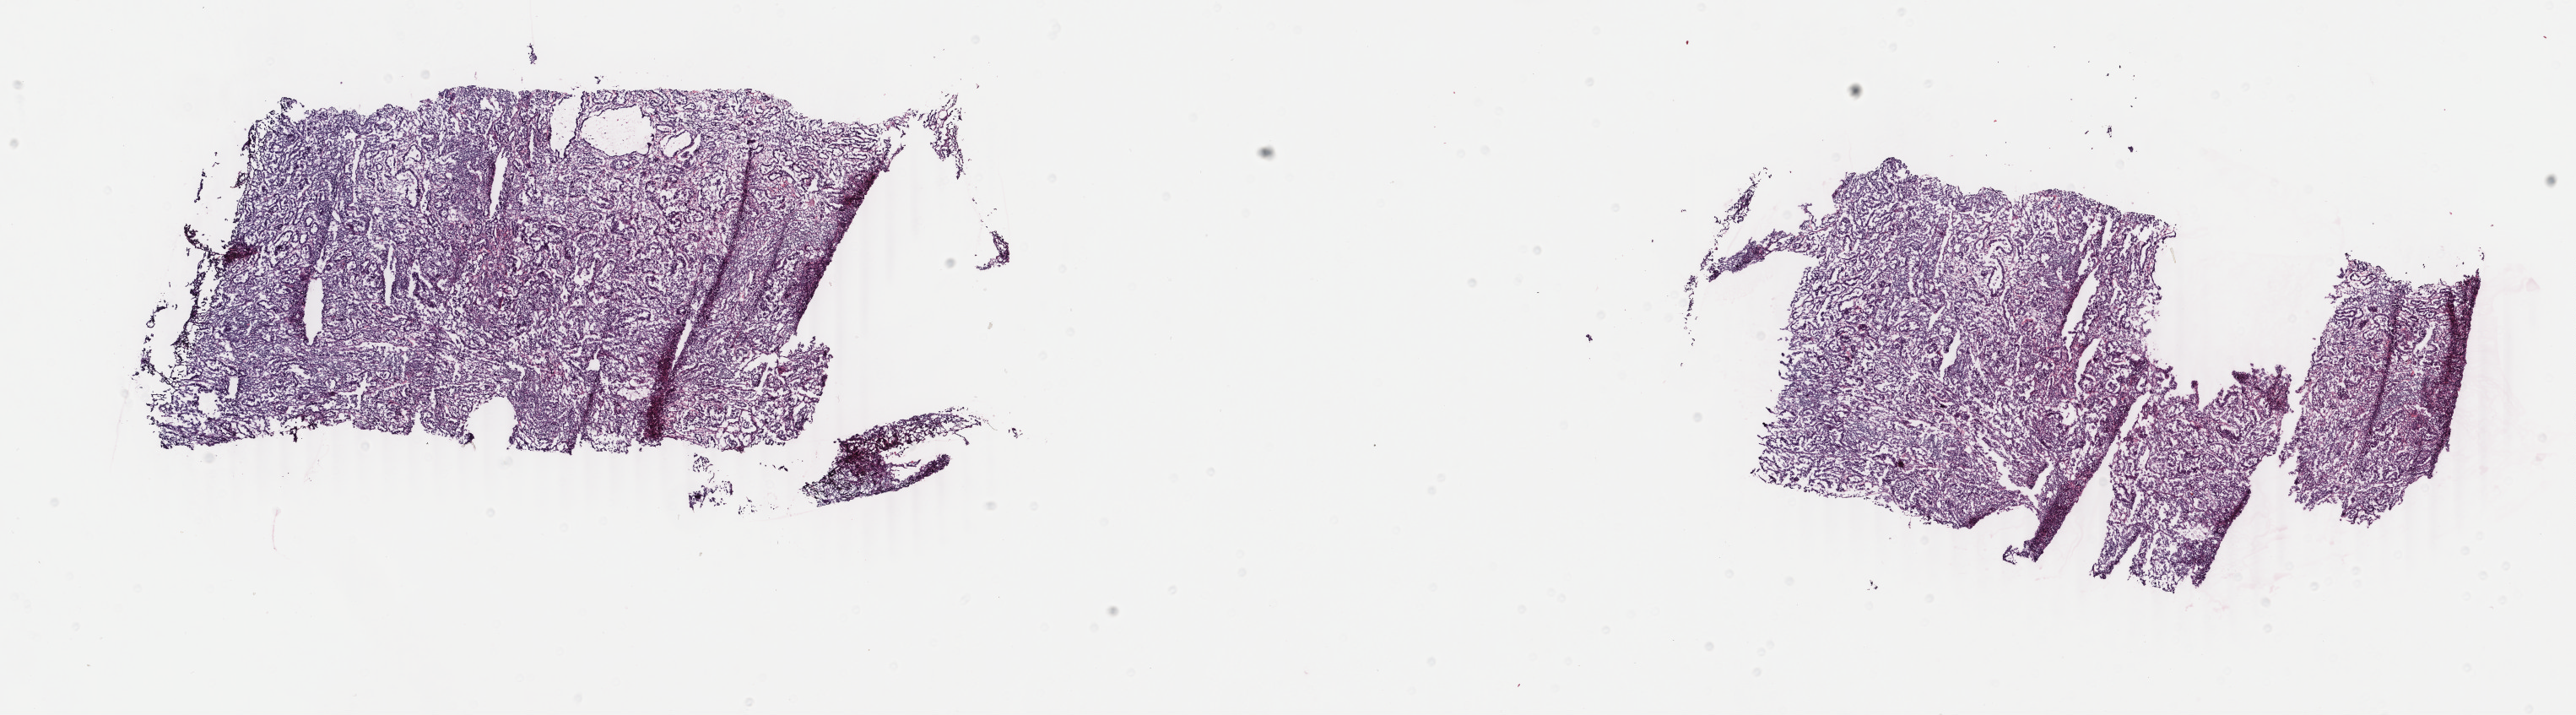
Whole-slide histology image, H&E-stained — low-resolution overview of the scanned area, about 24.3 x 6.7 mm (from a 40x scan). Frozen section. Sample: primary tumour, uterus. Female patient; age at initial diagnosis 69 years.
Diagnosis: Endometrioid adenocarcinoma, NOS (endometrium).